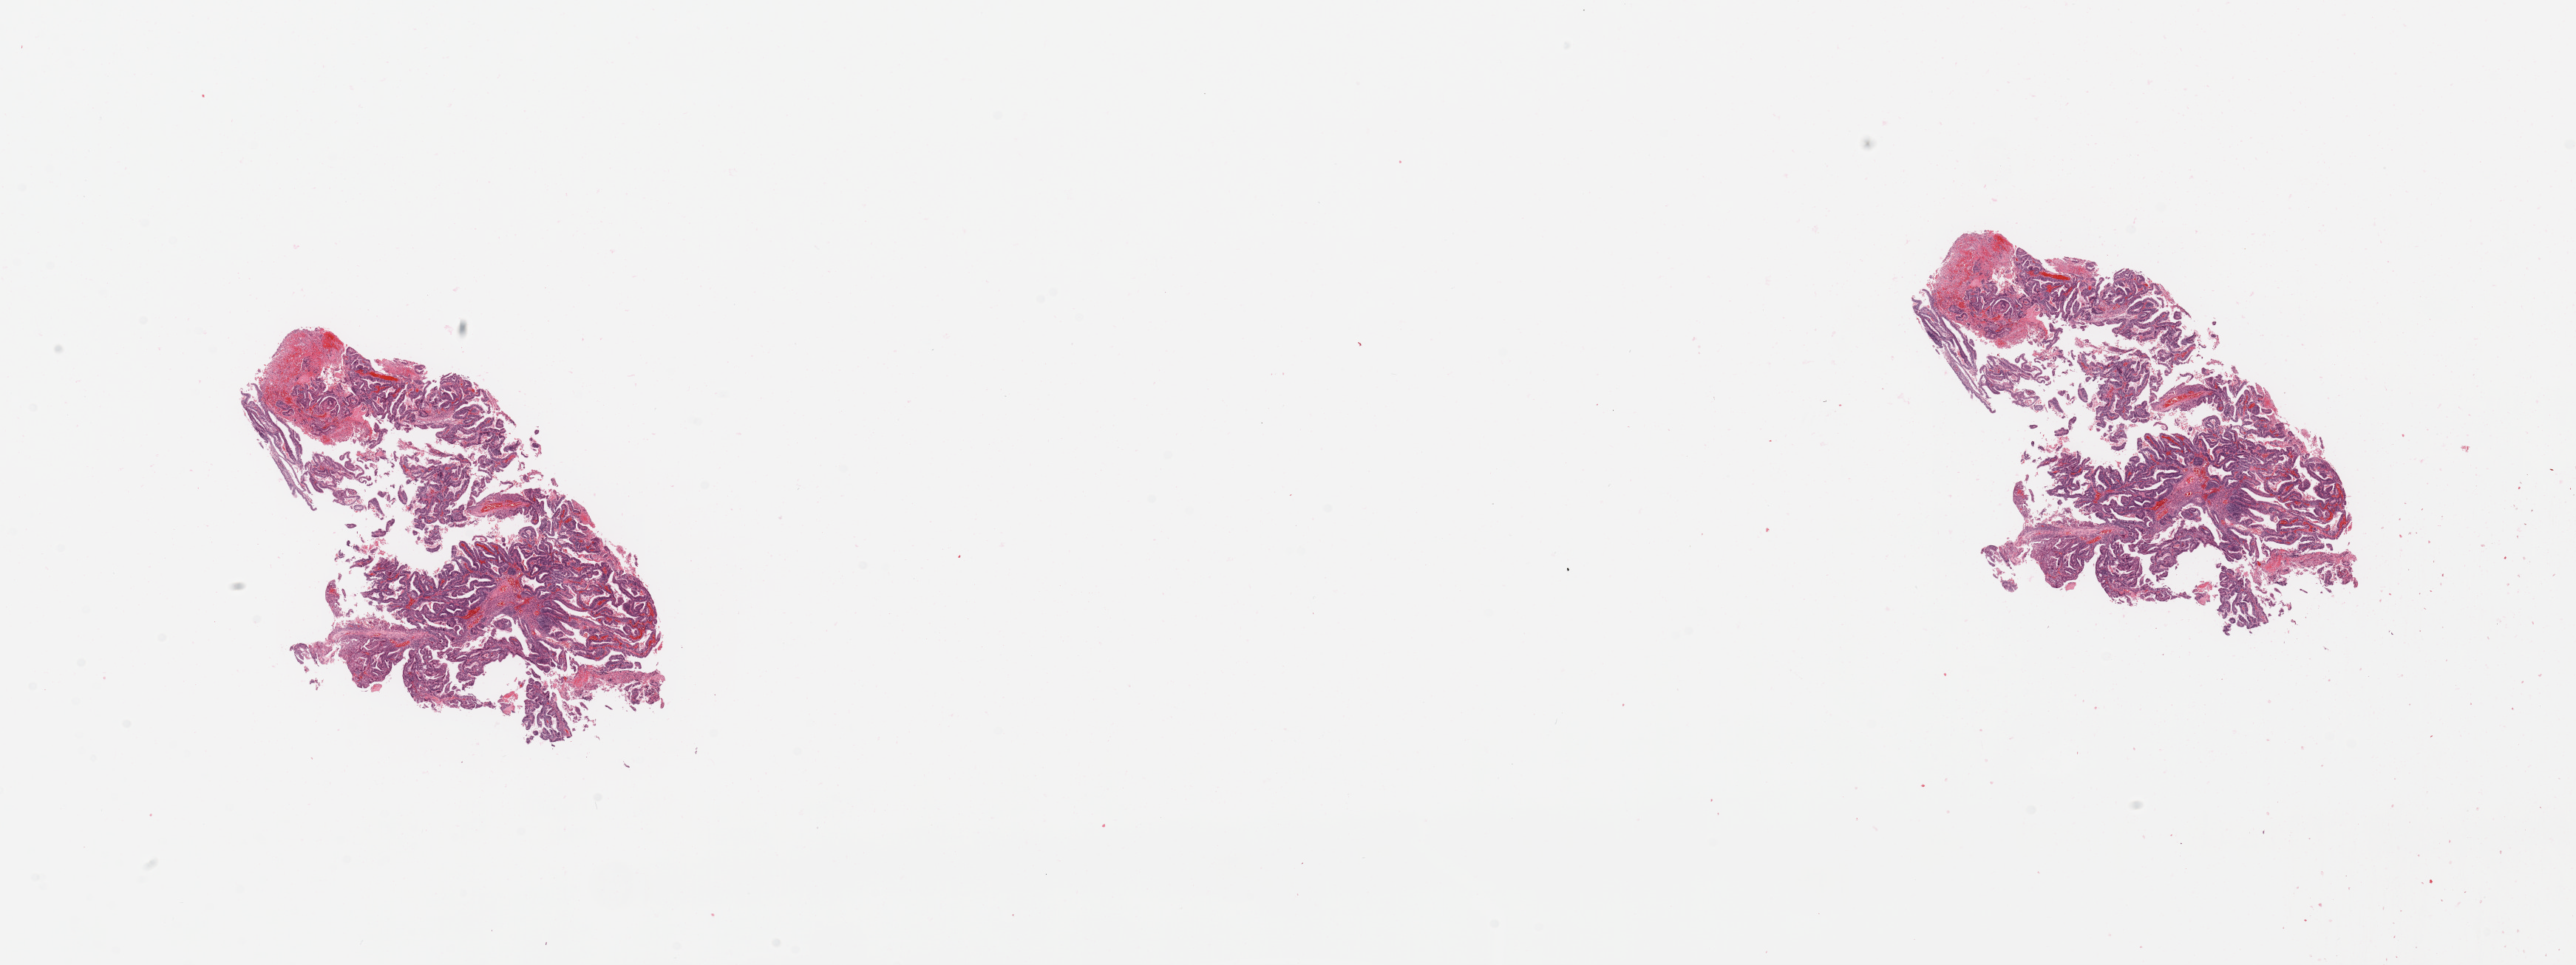
Hematoxylin and eosin (H&E) stained whole-slide image, shown as a low-resolution overview of the whole scanned area (about 27.6 x 10.3 mm). Tumour tissue sample, sampled site: uterus. Patient: female, age 61 years. Histologic grade: G2 (moderately differentiated). Pathologist review of this section (percent, as recorded): tumour nuclei 85%, necrosis 0%.
Histologic diagnosis: Endometrioid adenocarcinoma, NOS. AJCC pathologic stage: II.